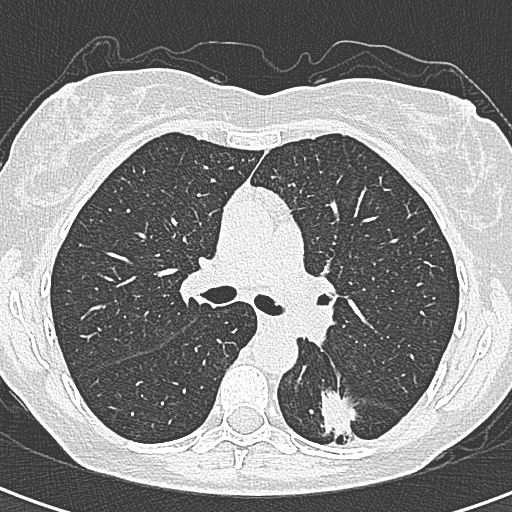
Low-dose screening chest CT, axial slice, first (baseline) screen, lung window (W 1500 / L -600 HU), slice 122 of 328 in the series. Female participant, aged 58 years at enrolment. Former smoker at enrolment.
- Lesion marked by an expert reader, box from (x=292, y=390) to (x=362, y=455) px.
- The screening reader recorded 2 non-calcified nodules or masses ≥4 mm on this exam (left lower lobe, right lower lobe); which of them this box marks is not recorded.
- Participant outcome: lung cancer diagnosed 22 days after this screen — adenocarcinoma, NOS, left lower lobe, moderately differentiated (G2), stage IA (AJCC 6th edition), 25 mm at pathology.